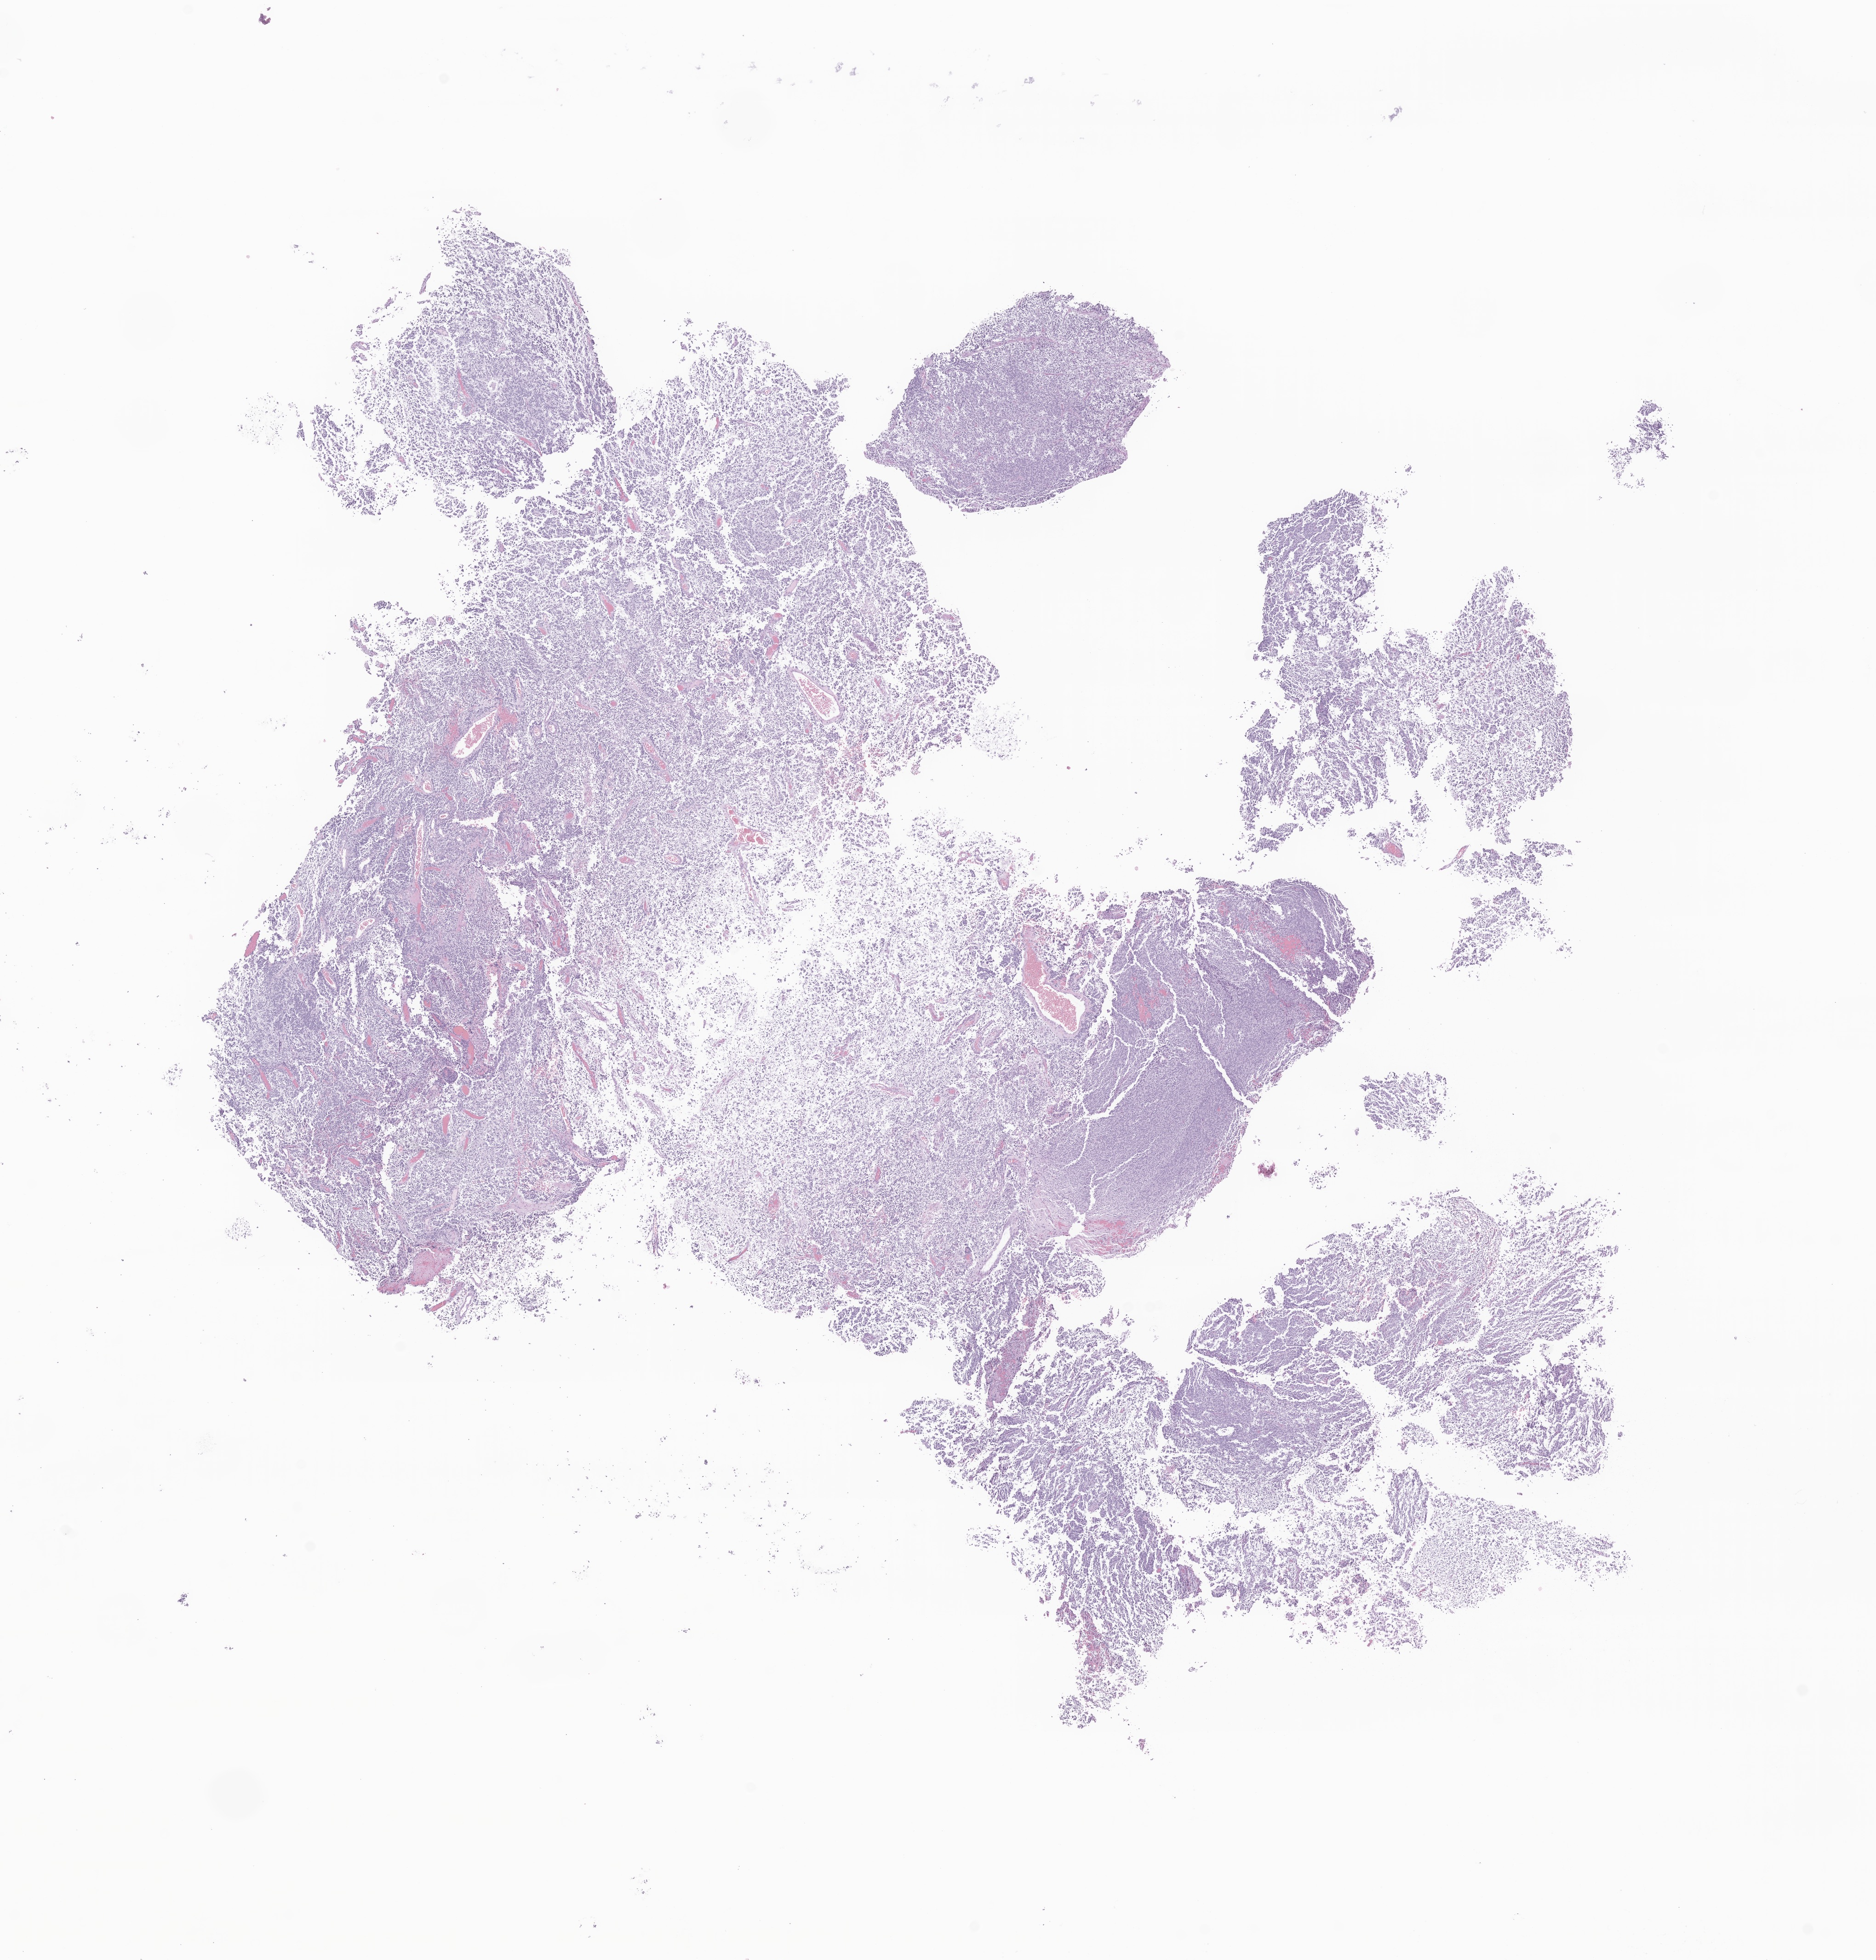
Whole-slide image, haematoxylin and eosin stain of tumor tissue from the brain, whole scanned area (about 17.2 x 18.0 mm) shown as a low-resolution overview, formalin-fixed, paraffin-embedded (FFPE) tissue. Patient: male, age 59 months (4 years 11 months).
Diagnosis: Neuroblastoma, NOS.